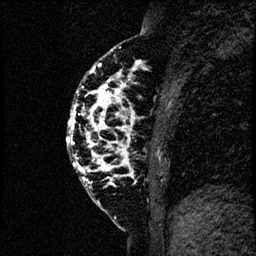
Breast MRI (dynamic contrast-enhanced), one sagittal slice. Slice 27 of 60 in the series (ordered by position). Dynamic contrast-enhanced study with each time point stored as its own series, time point 2 of 4 at this slice position (early post-contrast, ordered by acquisition time). 1.5 T. TE 4.2 ms, TR 17.6 ms. 2 mm slice thickness. 256 × 256 image matrix, field of view 200 × 200 mm. Patient: female, 40 years. Case-level facts recorded for this patient, not image findings: setting: breast cancer imaged before/during neoadjuvant chemotherapy; receptor status: HER2-positive.
Annotated regions visible in this slice (semi-automatic segmentation, software-assisted and operator-edited):
- analysis volume of interest (the breast-tissue region the enhancement analysis was run in; not a lesion): box from (x=66, y=55) to (x=184, y=206) px
- tumour enhancement mask (voxels above the 100 % enhancement threshold inside the analysis volume of interest): (x=66, y=62)–(x=138, y=187)